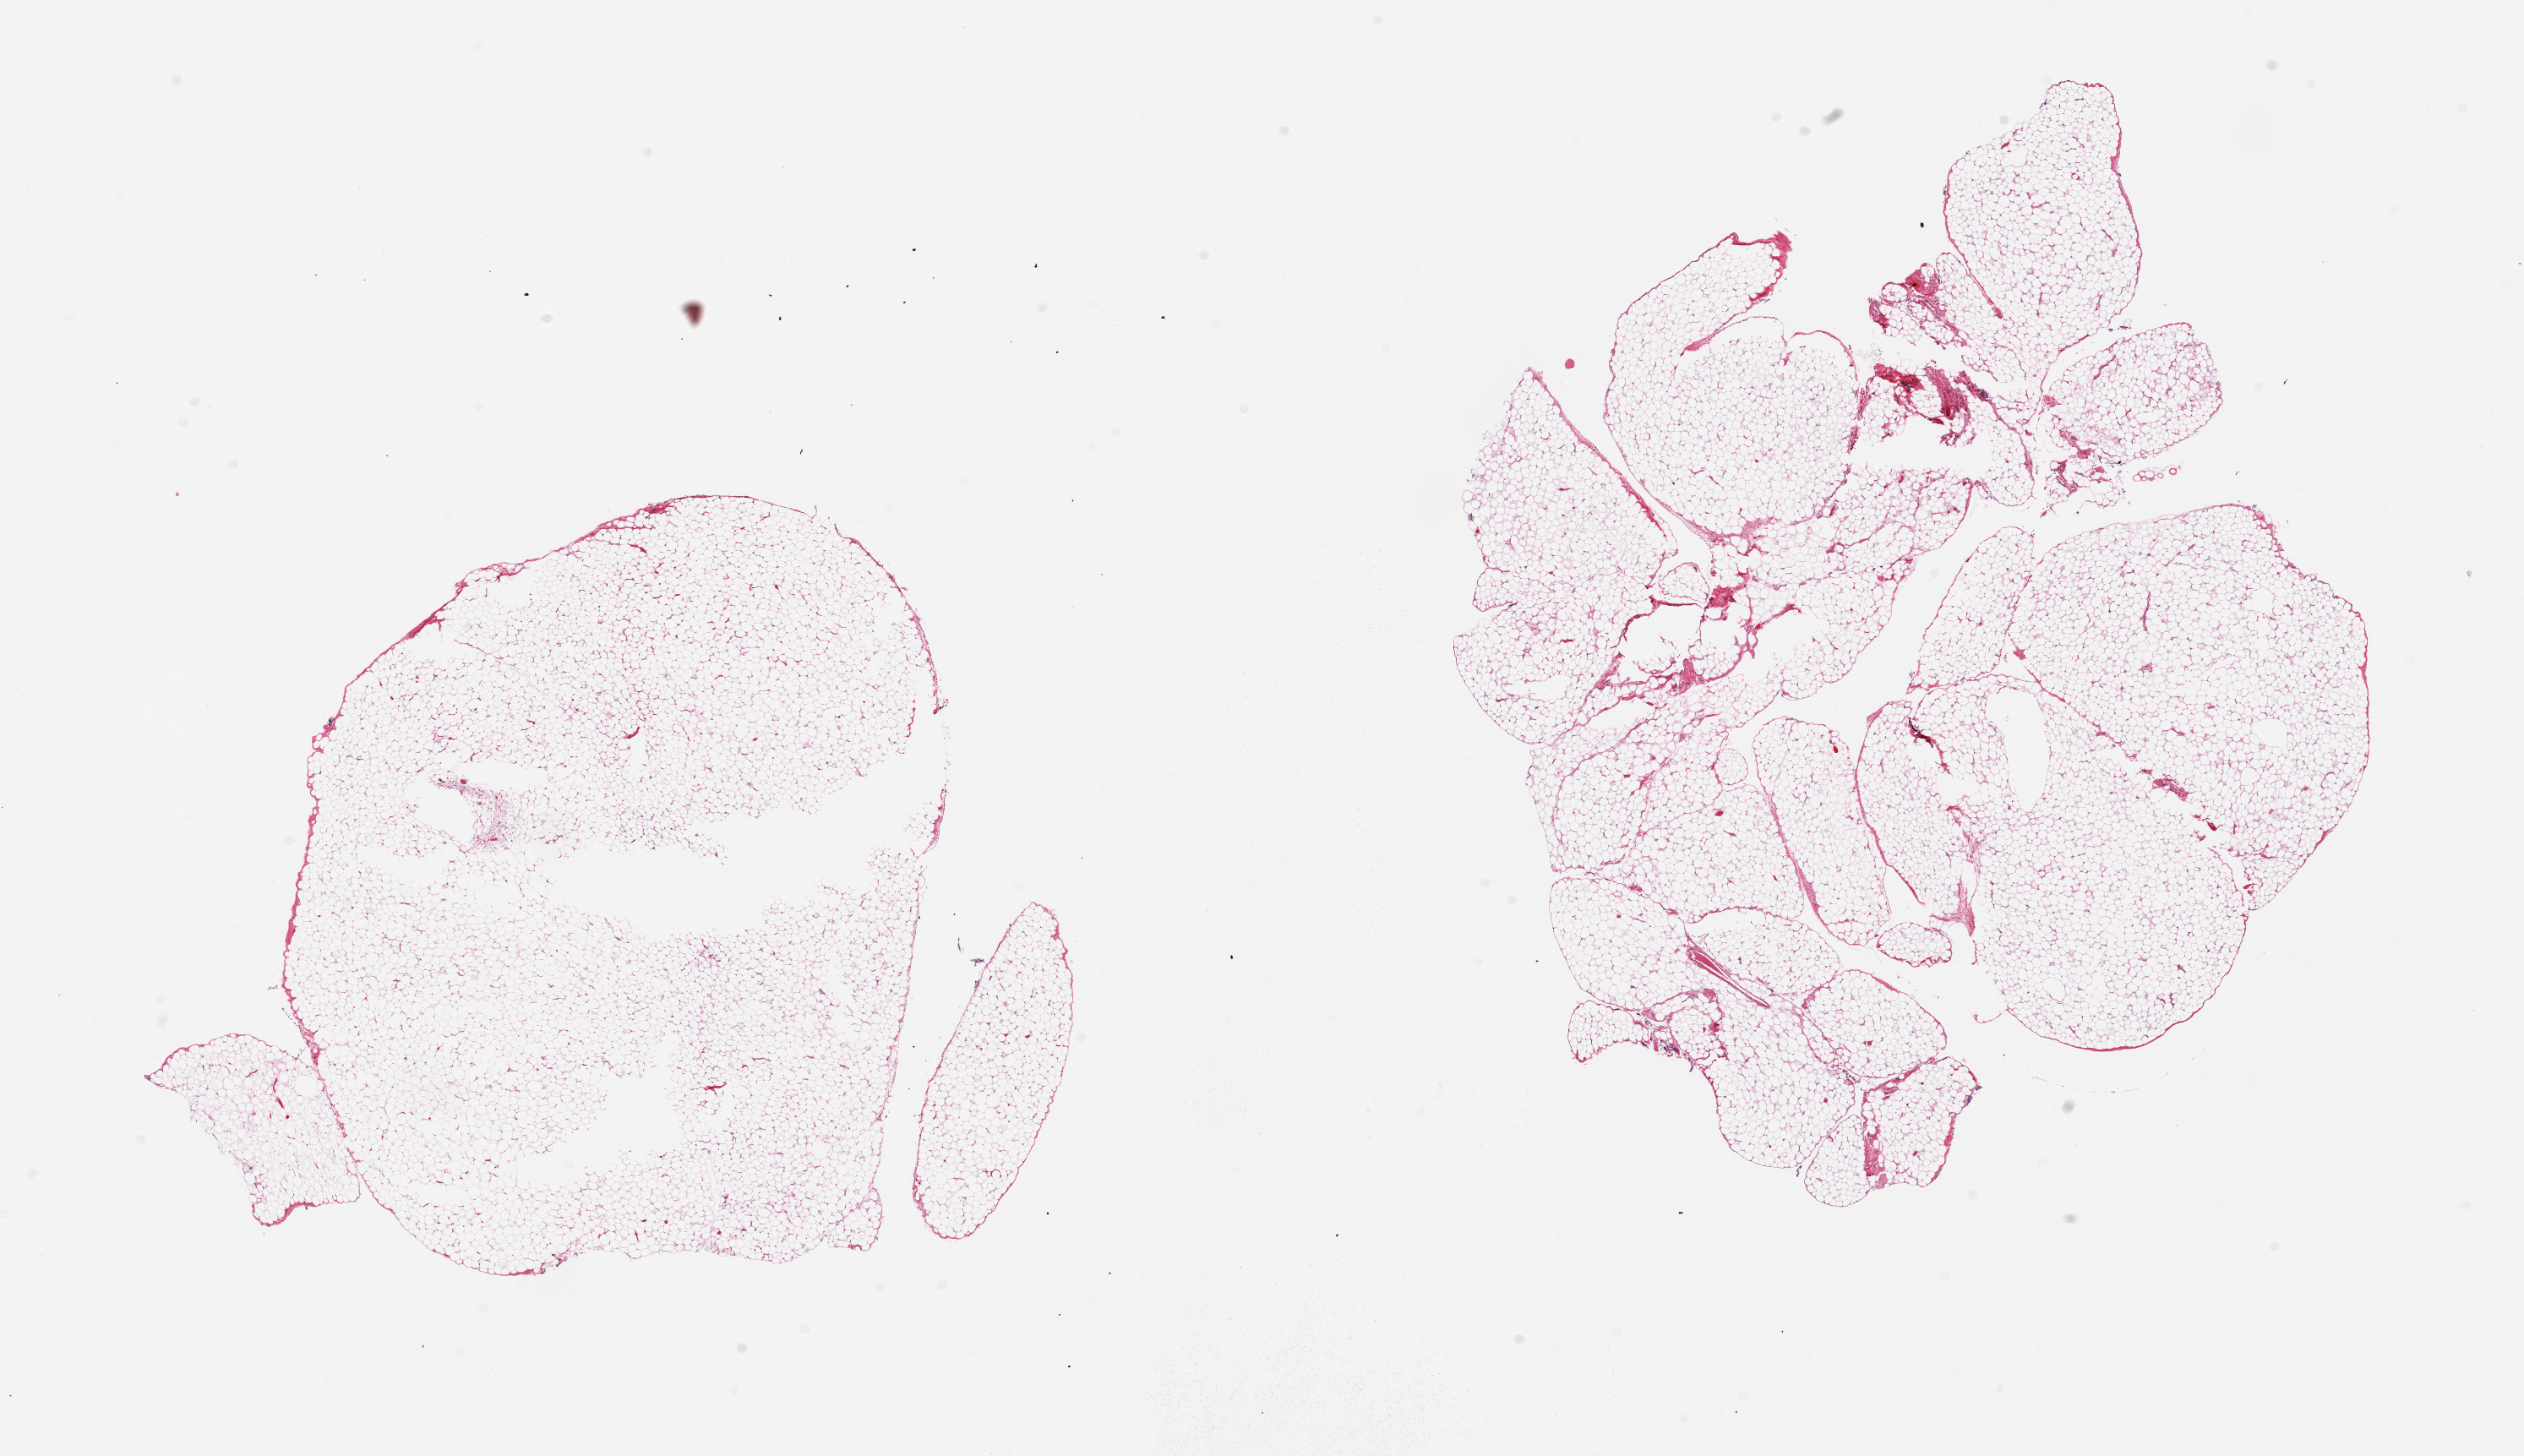
Whole-slide image, hematoxylin and eosin (H&E) stain, low-resolution overview of the scanned area, about 23.6 x 13.6 mm; PAXgene-fixed paraffin-embedded (PFPE) section; target tissue: omentum; donor tissue sample. Donor: male.
• pathologist's review note for this sample: 2 pieces; minimal fibrous content